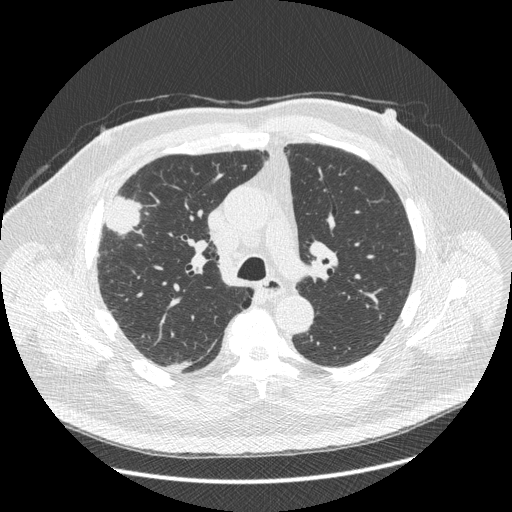
Low-dose screening chest CT, axial slice, third screening round (two years after baseline), lung window (W 1500 / L -600 HU), 1.25 mm slice thickness, standard (soft-tissue) reconstruction kernel (STANDARD), slice 145 of 426 in the series. Male, age 66 years at enrolment. Current smoker at enrolment.
Lesion marked by an expert reader, bounding box [x1, y1, x2, y2] px = [86, 186, 145, 266]. Screening reader's record for this exam (one nodule recorded; not confirmed to be the boxed lesion): non-calcified nodule or mass ≥4 mm, right upper lobe, 48 × 25 mm, spiculated (stellate) margins, soft tissue attenuation, pre-existing on the prior screen: no. Lung cancer was diagnosed 35 days after this screen: non-small cell carcinoma, right upper lobe, stage IV (AJCC 6th edition), 50 mm at pathology.